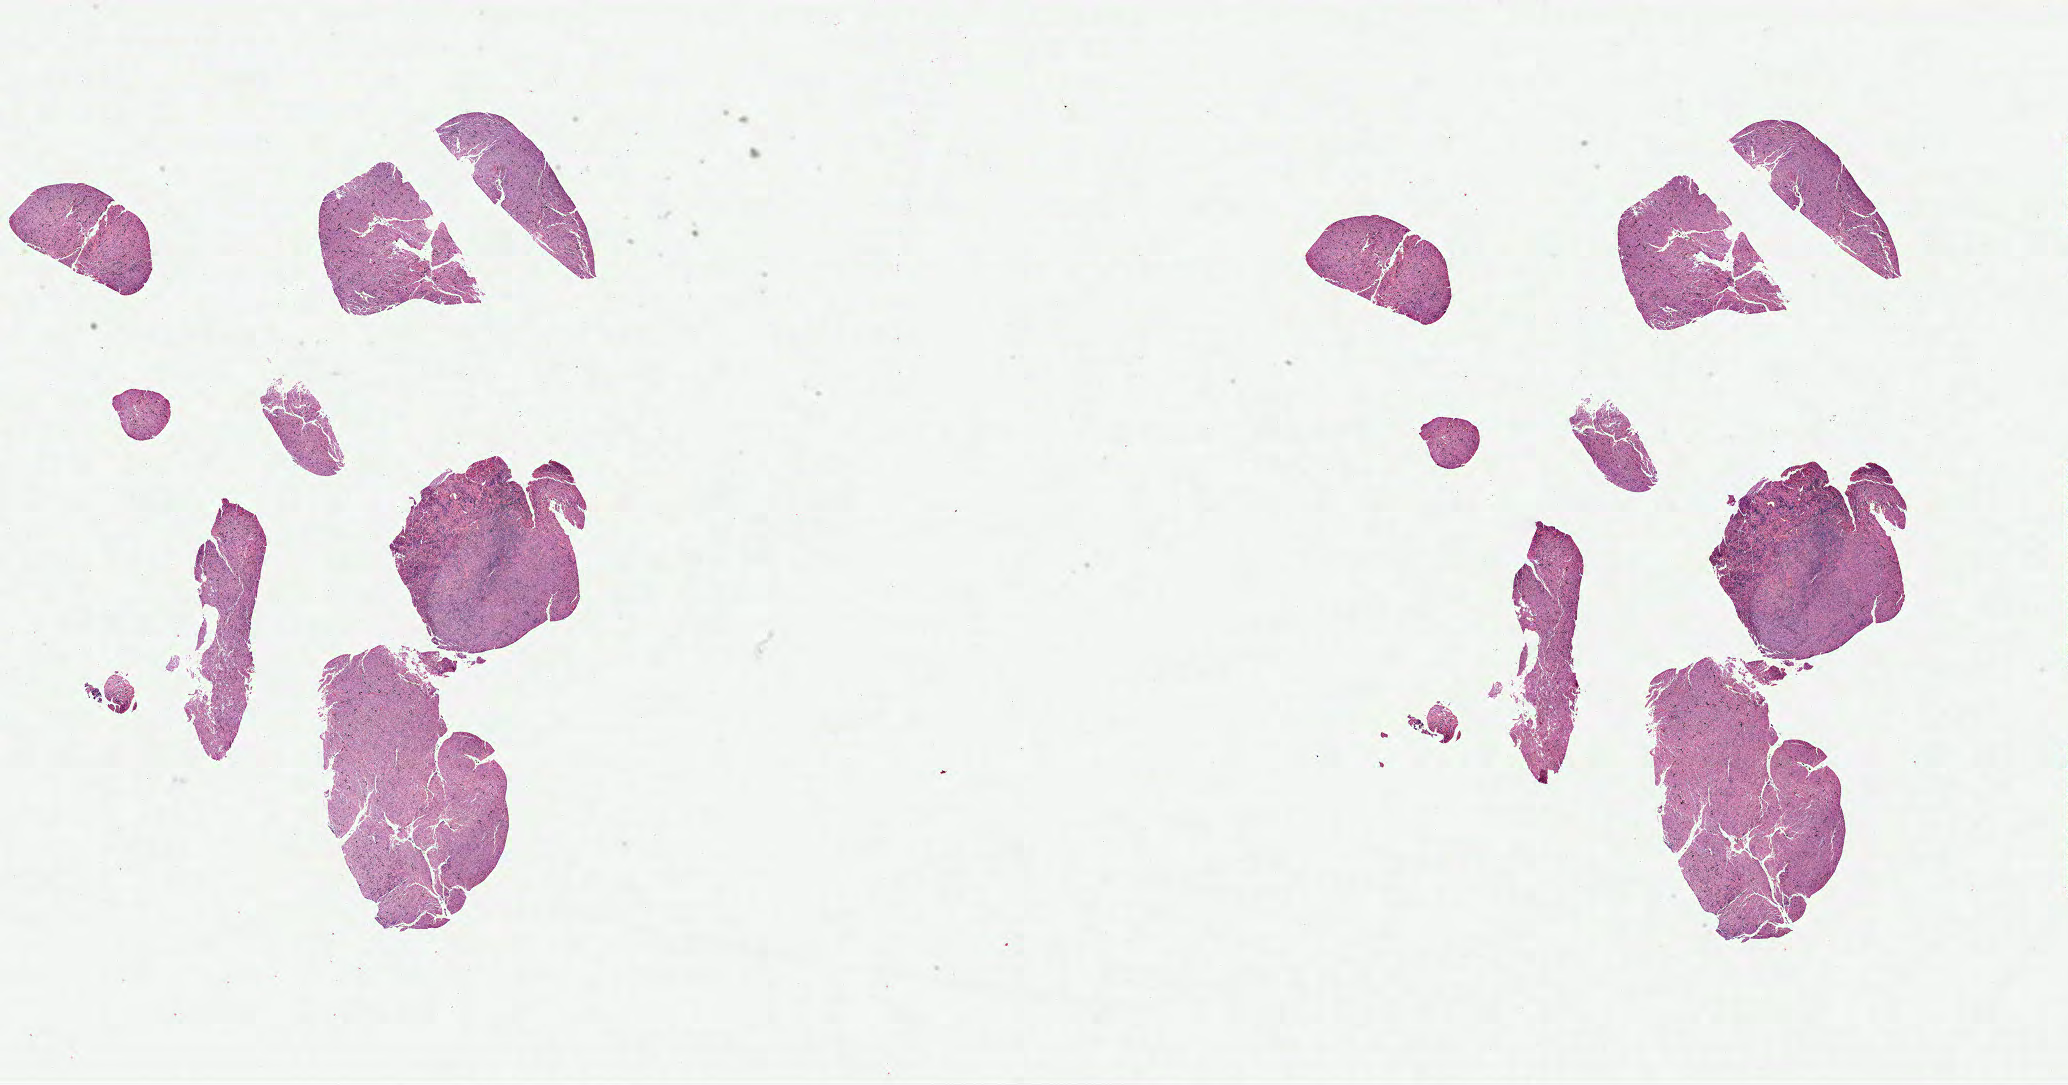
Whole-slide histology image, H&E-stained, a low-resolution overview of the entire scanned area, about 33.4 x 17.5 mm (slide scanned at 40x). FFPE section. Primary tumour sample from the lymphoid tissue. Male, age 67 years at initial diagnosis.
Diagnosis: Diffuse large B-cell lymphoma, NOS (intrathoracic lymph nodes).